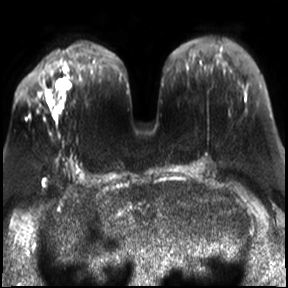
Breast MRI, one axial slice; position 11 of 30 along the scan axis; diffusion-weighted series; image 2 of 4 stored at this slice position (different b-values; order by instance number); 3 T; 288 × 288 image matrix, field of view 340 × 340 mm. Female patient.
Outlined on this slice (outlined manually by an expert reader):
- tumour on diffusion-weighted imaging: box from (x=44, y=78) to (x=71, y=110) px